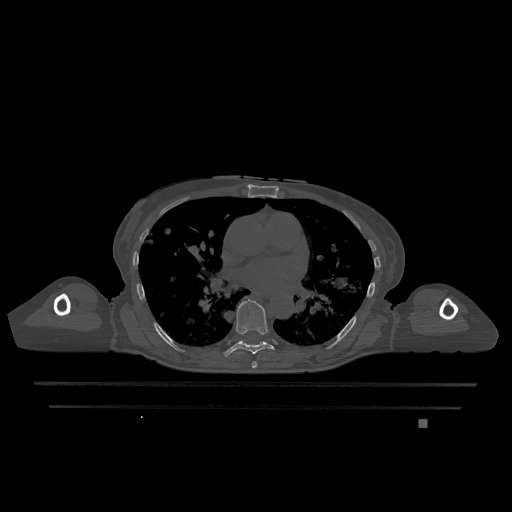
CT including the spine, one axial slice; slice 737 of 1317 in the series (ordered by position); bone window (W 1800 / L 400 HU); 0.5 mm slice thickness; 512 × 512 image matrix. Female patient, age 74 years. Case-level facts recorded for this patient, not image findings: primary cancer: lung.
Outlined on this slice (semi-automatic segmentation, software-assisted and operator-edited):
- T6 vertebra: bounding box [x1, y1, x2, y2] px = [252, 361, 258, 368]
- T7 vertebra: [223, 299, 274, 357]